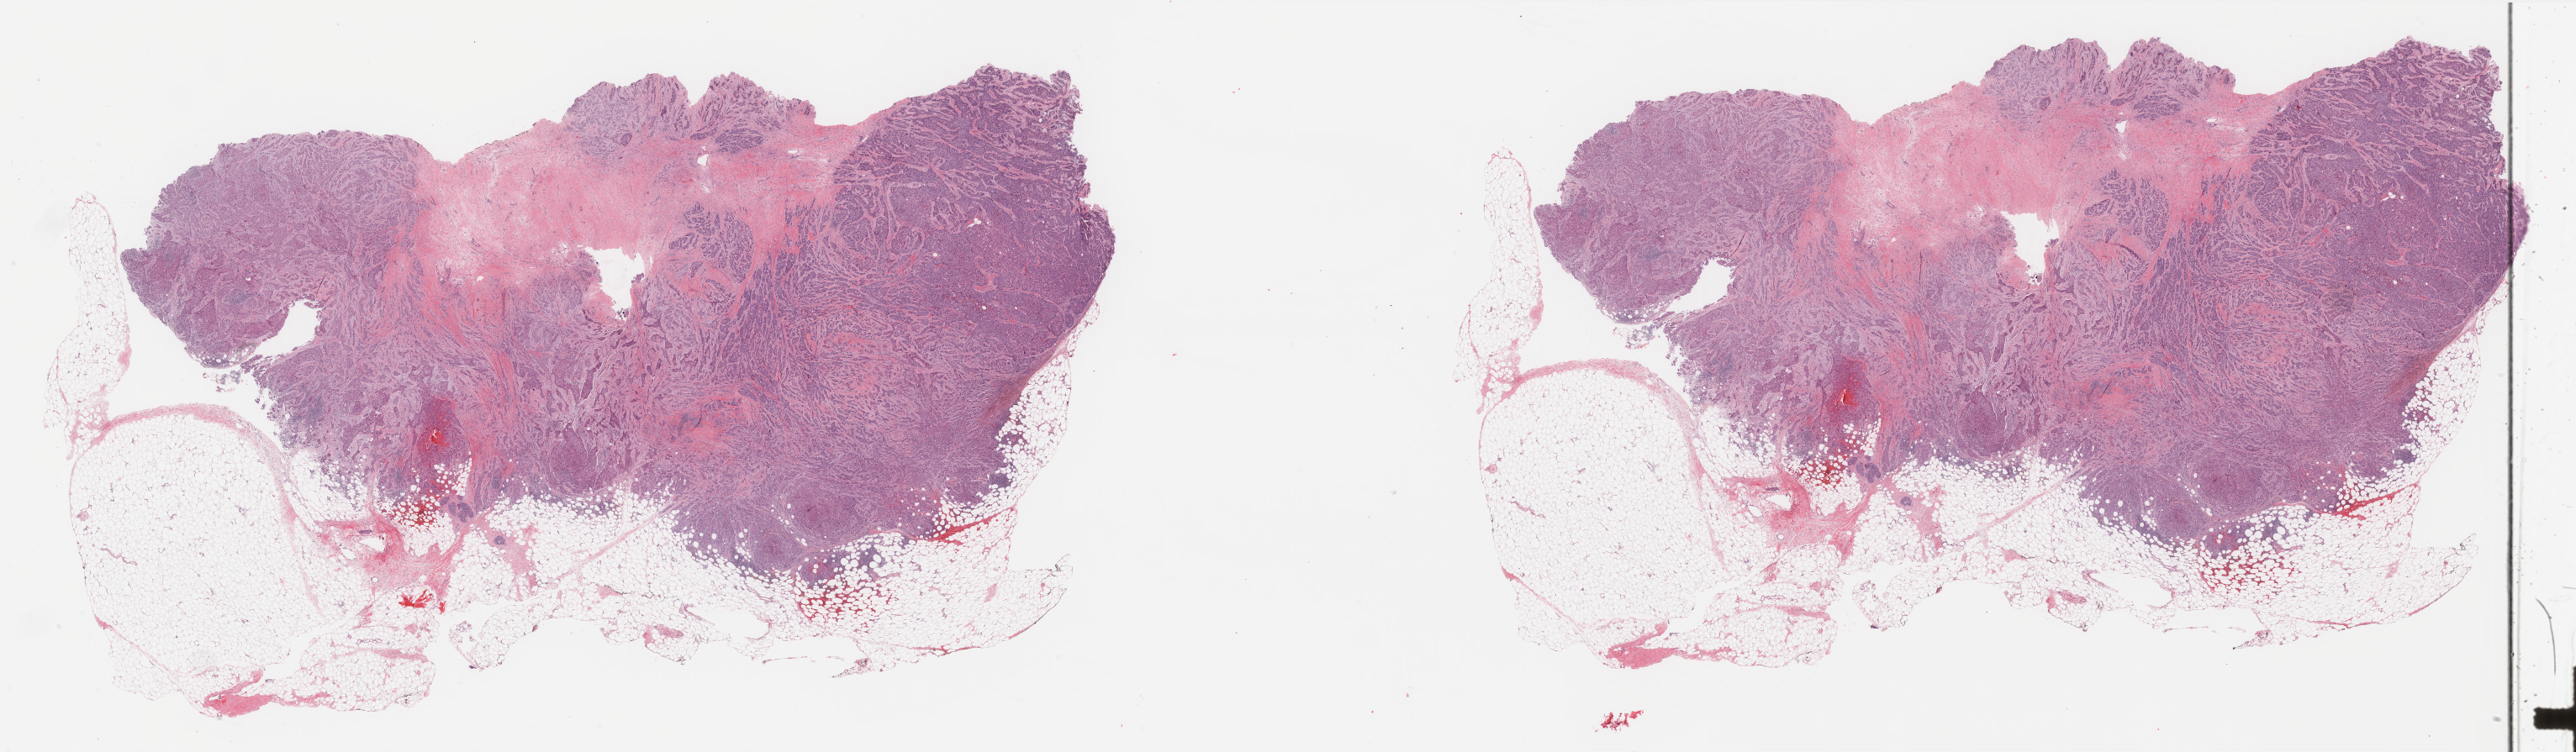
Digitized H&E tissue section (whole slide) — whole scanned area (about 48.5 x 14.2 mm) shown as a low-resolution overview. Formalin-fixed paraffin-embedded (FFPE) diagnostic section. Breast, primary tumour sample. Male patient; age at initial diagnosis 51 years.
Histologic diagnosis: Infiltrating duct carcinoma, NOS.